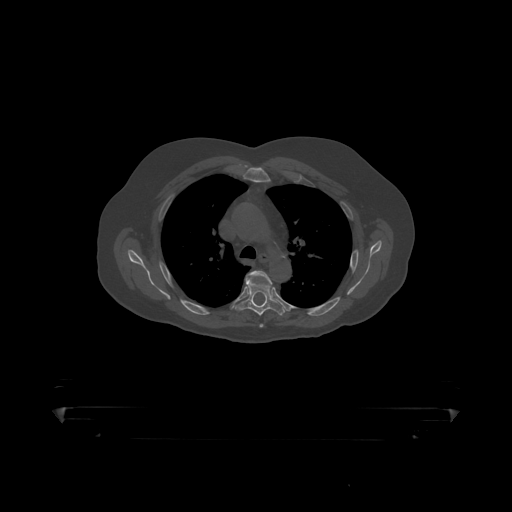
CT including the spine, one axial slice; position 325 of 390 along the scan axis; bone window (W 1800 / L 400 HU); 1.25 mm slice thickness; 512 × 512 image matrix, field of view 650 × 650 mm. Patient: male, 60 years. Case-level facts recorded for this patient, not image findings: primary cancer: prostate.
Annotated regions visible in this slice (semi-automatically segmented with operator editing):
- T4 vertebra: box from (x=246, y=271) to (x=272, y=284) px
- T5 vertebra: (x=235, y=279)–(x=287, y=317)